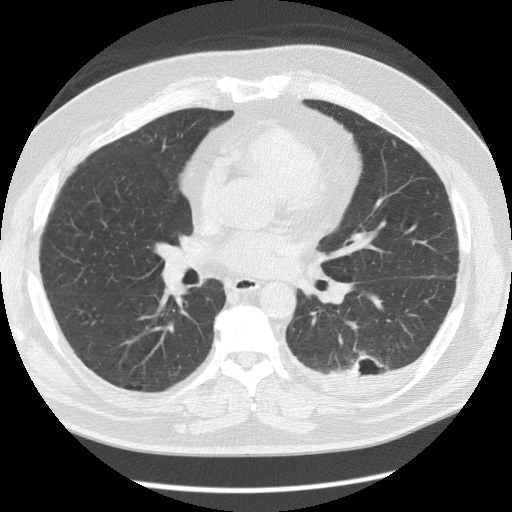
Chest CT (low-dose screening protocol), one axial image. First (baseline) screen. Lung window (W 1500 / L -600 HU). Slice 61 of 126 in the series. Male participant, aged 56 years at enrolment.
• Expert reader's lesion annotation, bounding box (x1, y1, x2, y2) in pixels: (325, 342, 397, 394).
• The screening reader recorded 4 non-calcified nodules or masses ≥4 mm on this exam (left lower lobe, left lower lobe, right middle lobe, left upper lobe); which of them this box marks is not recorded.
• Official screen result: positive, change unspecified: nodule(s) >= 4 mm or enlarging nodule(s), mass(es), or other non-specific abnormalities suspicious for lung cancer.
• Later outcome: lung cancer diagnosed 173 days after this screen — non-small cell carcinoma, left lower lobe, stage IV (AJCC 6th edition), 50 mm at pathology.